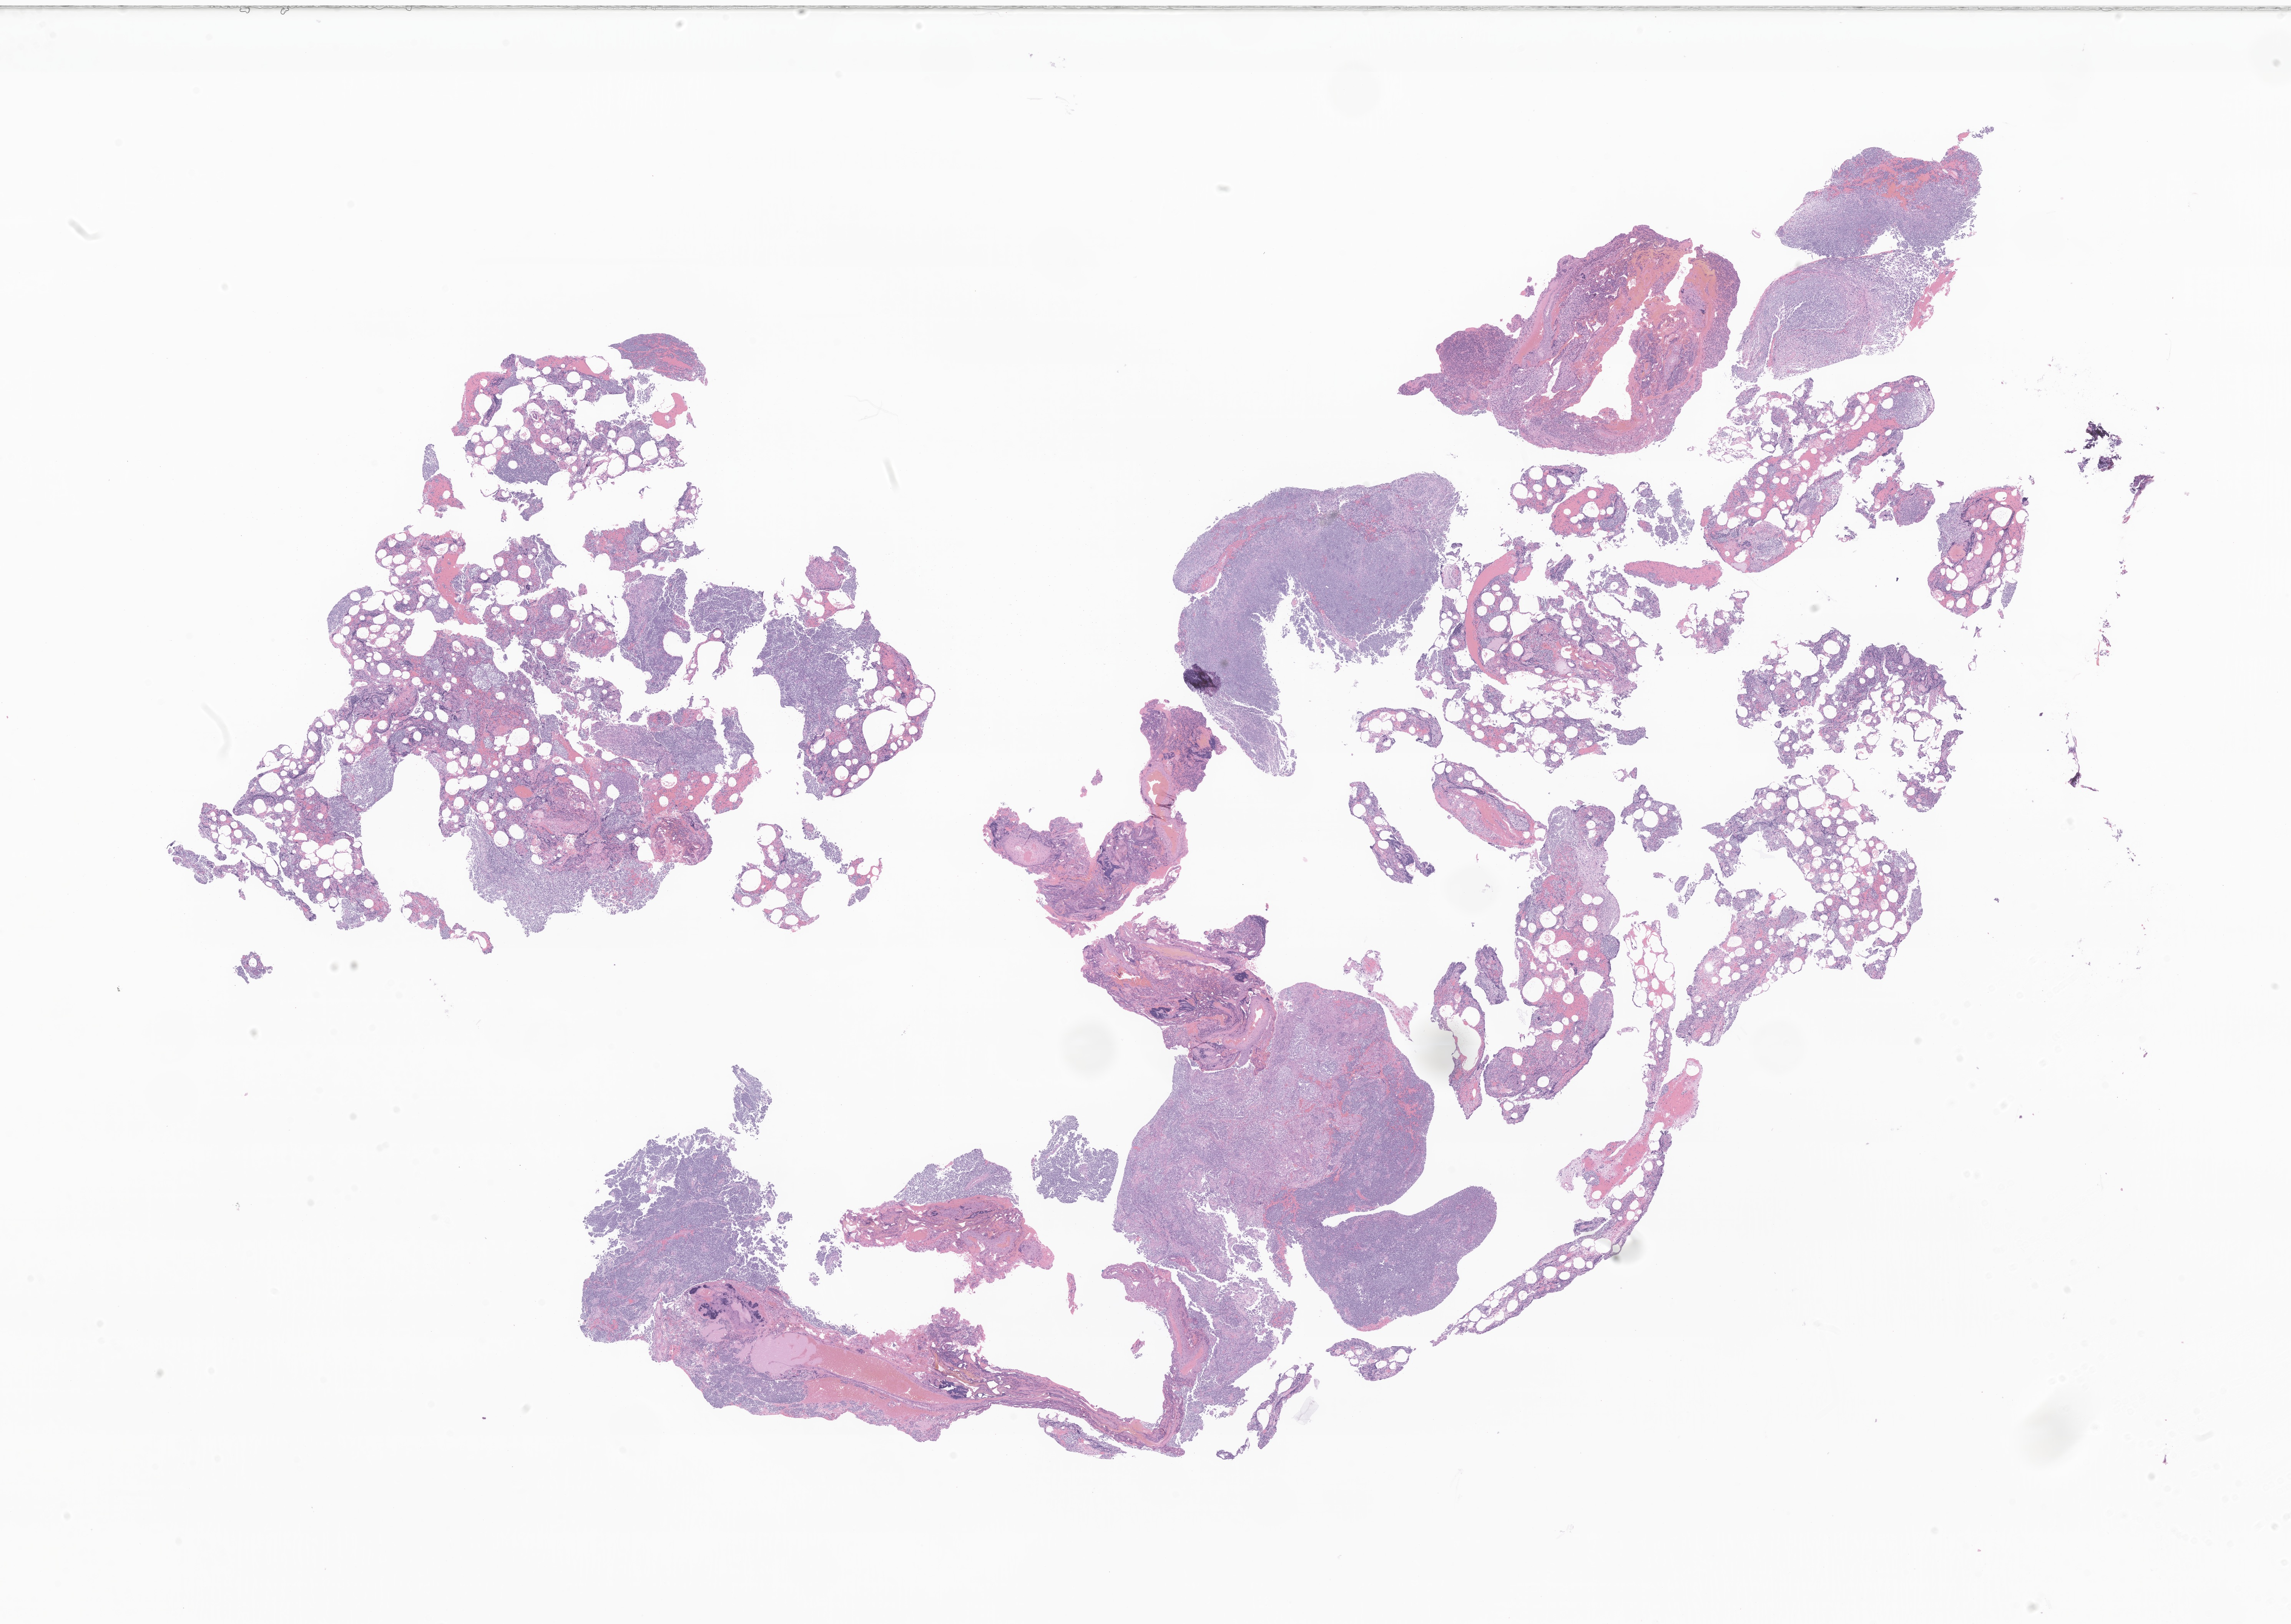
Whole-slide image, haematoxylin and eosin stain of tumor tissue from the brain — whole scanned area (about 25.1 x 17.8 mm) shown as a low-resolution overview, formalin-fixed, paraffin-embedded (FFPE) tissue. Patient: male, age 53 months (4 years 5 months).
• diagnosis (ICD-O-3 morphology term): Medulloblastoma, NOS